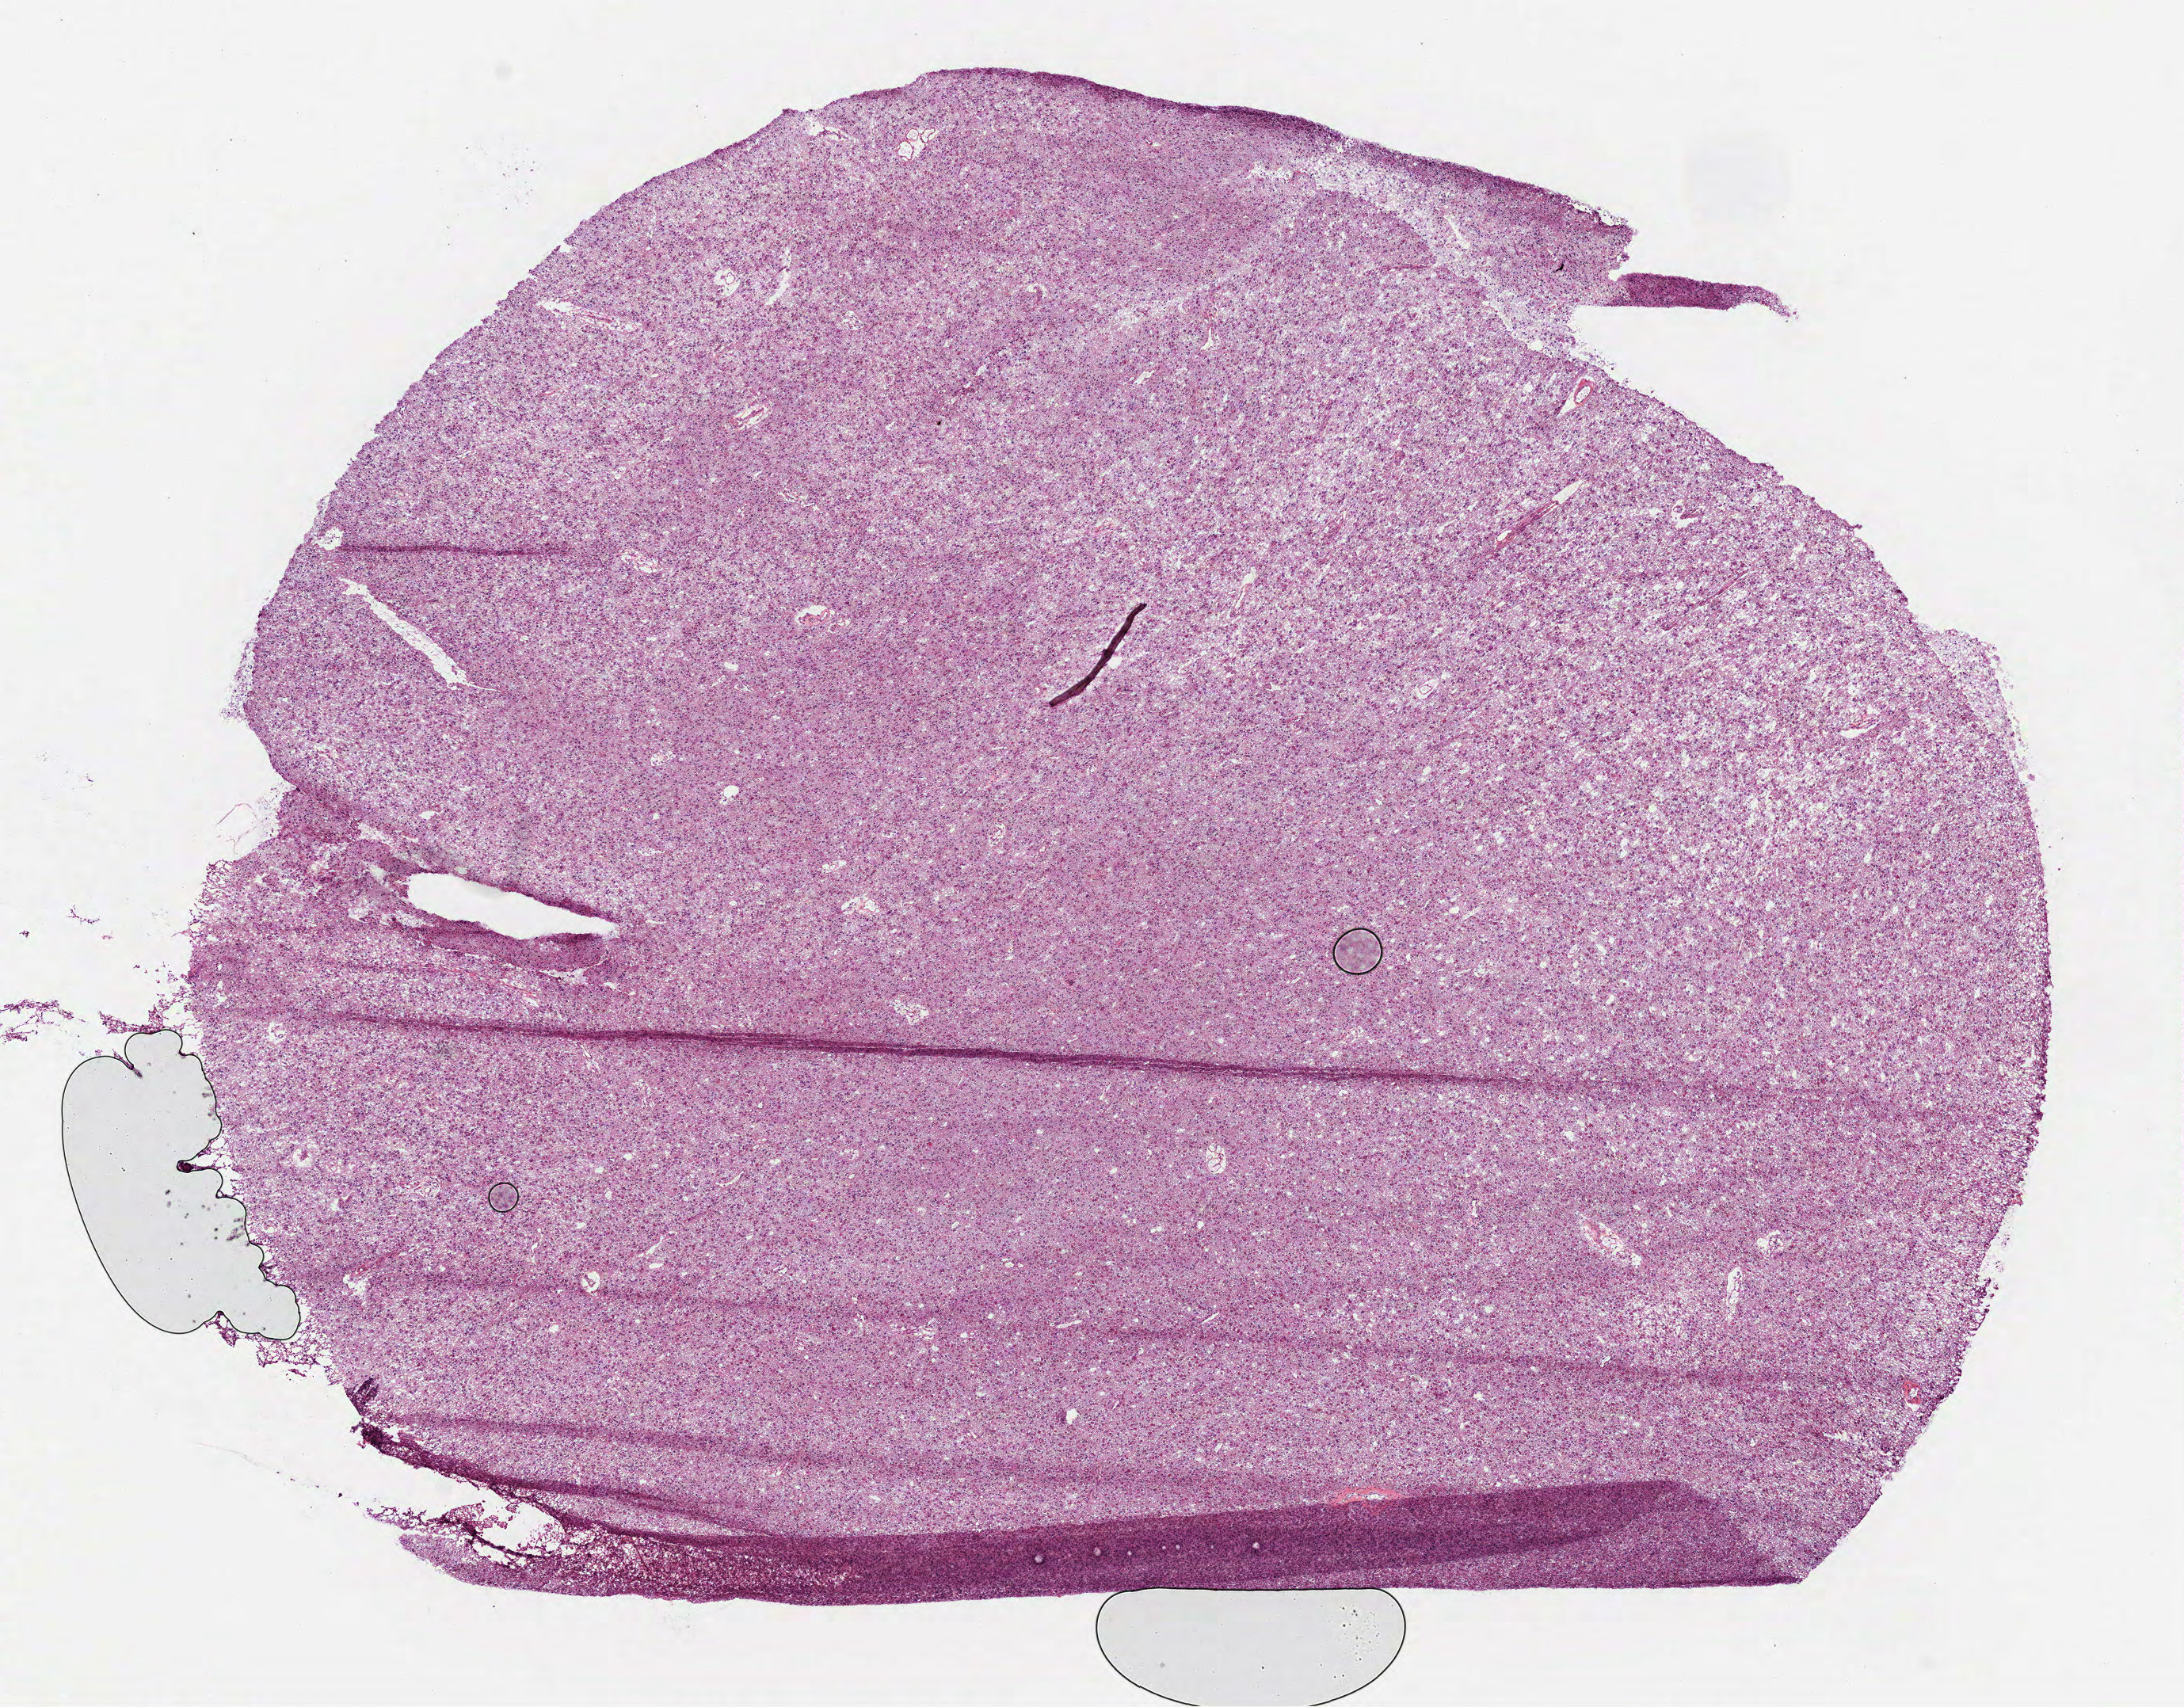
H&E whole-slide image — shown as a low-resolution overview of the whole scanned area (about 11.1 x 8.7 mm, acquisition: 40x scan), frozen section from the bottom of the tissue portion, sample: primary tumour, brain. Male, age 67 years at initial diagnosis. Histologic grade: G2 (moderately differentiated). Slide review estimates, as recorded: tumour cells 100%, tumour nuclei 75%, normal cells 0%, stromal cells 0%, necrosis 0%.
Laterality: right. Diagnosis: Mixed glioma (cerebrum).